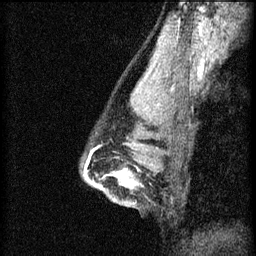
Breast MRI (dynamic contrast-enhanced), one sagittal slice; slice 44 of 60 in the series (ordered by position); 3 images stored at this slice position (order not interpretable as contrast timing); 1.5 T; TE 4.2 ms, TR 8.2 ms; 2 mm slice thickness; 256 × 256 image matrix, field of view 180 × 180 mm. Patient: female, 44 years.
Outlined on this slice (semi-automatically segmented with operator editing):
- analysis volume of interest (the breast-tissue region the enhancement analysis was run in; not a lesion): bounding box [x1, y1, x2, y2] px = [94, 164, 143, 205]
- tumour enhancement mask (voxels above the 70 % enhancement threshold inside the analysis volume of interest): [114, 172, 133, 187]